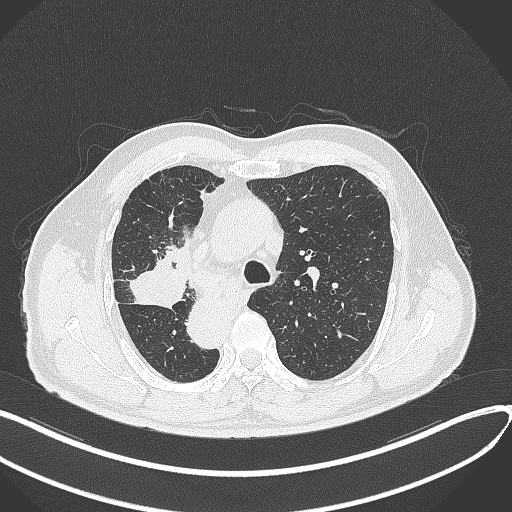
Chest CT, one axial slice. Slice 216 of 300 in the series (ordered by position). Lung window (W 1500 / L -600 HU). 512 × 512 image matrix, field of view 400 × 400 mm. Male patient, age 67 years. From the clinical record (not read from this slice): clinical TNM (as recorded): T2a N0 M0.
Annotated regions visible in this slice (bounding box drawn by a radiologist):
- lung tumour (recorded histology: squamous cell carcinoma): bounding box <124,263,191,312> (left, top, right, bottom; pixels)